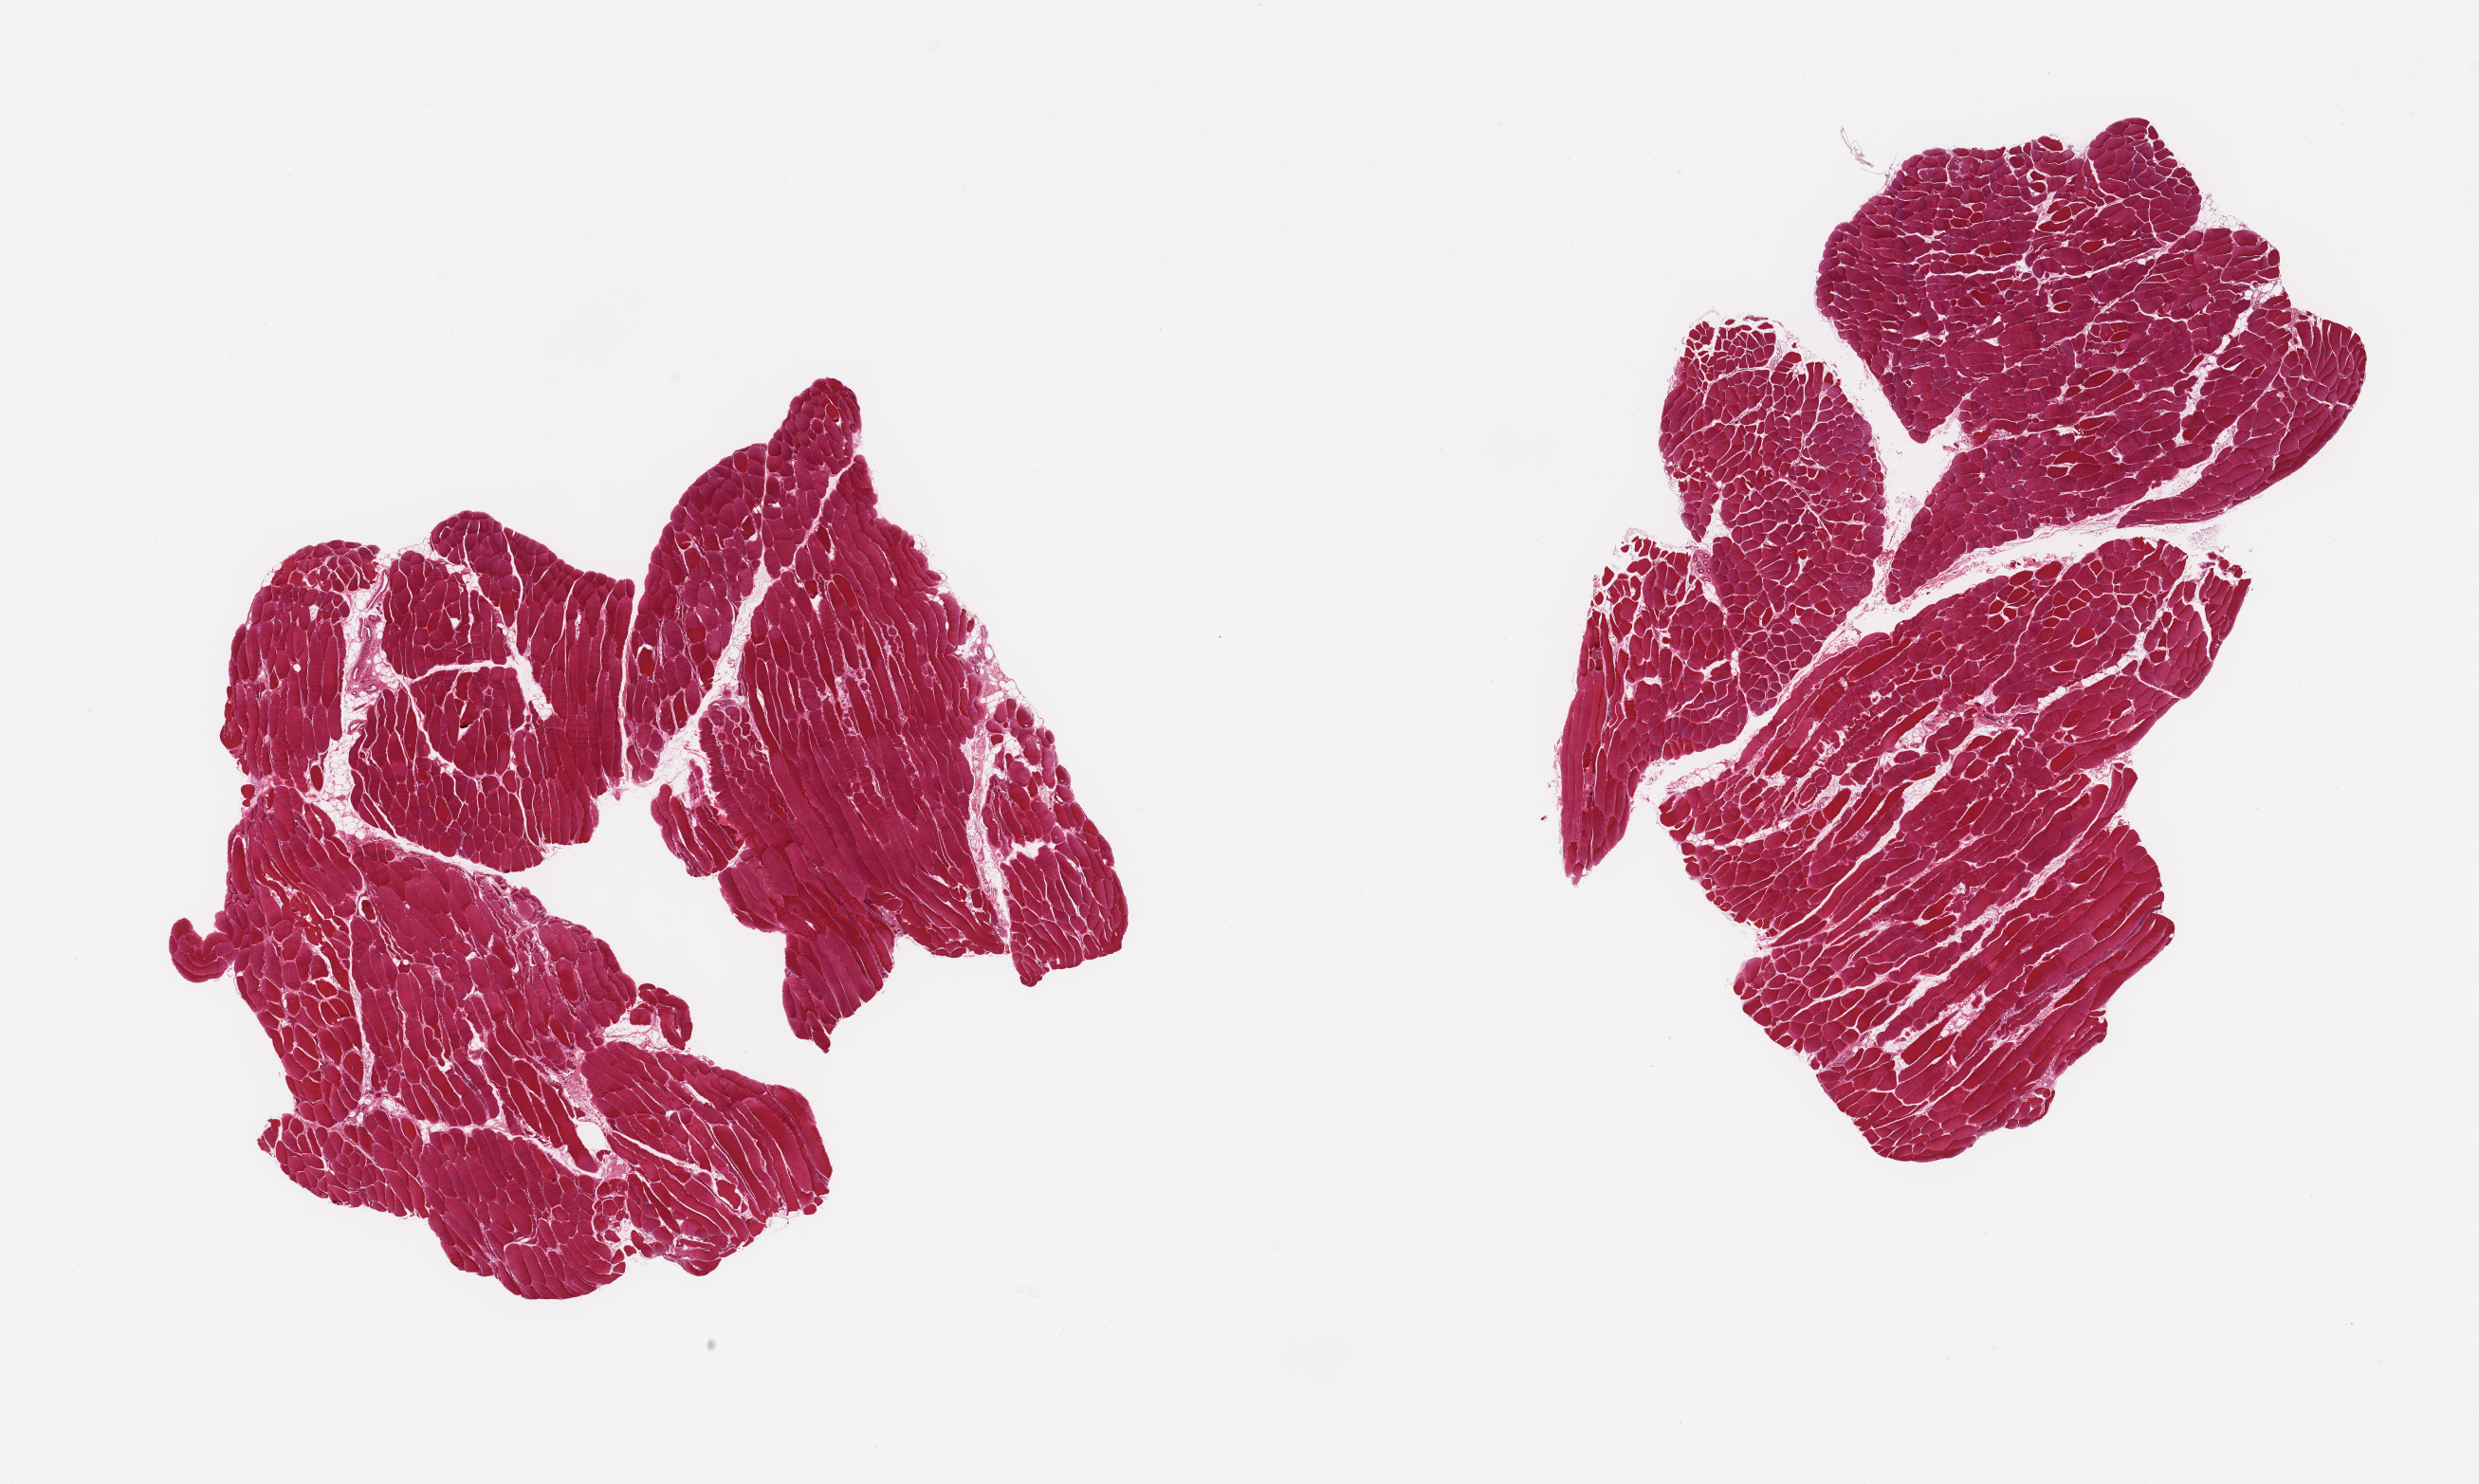
Whole-slide image, hematoxylin and eosin (H&E) stain, low-resolution overview of the scanned area, about 20.7 x 12.4 mm; PAXgene-fixed paraffin-embedded (PFPE) section; sampled site (target tissue): skeletal muscle; tissue donor sample. Donor sex: male.
- reviewer comment on this tissue sample: 2 pieces, interstitial fat/vascular elements are ~5-10% tissue